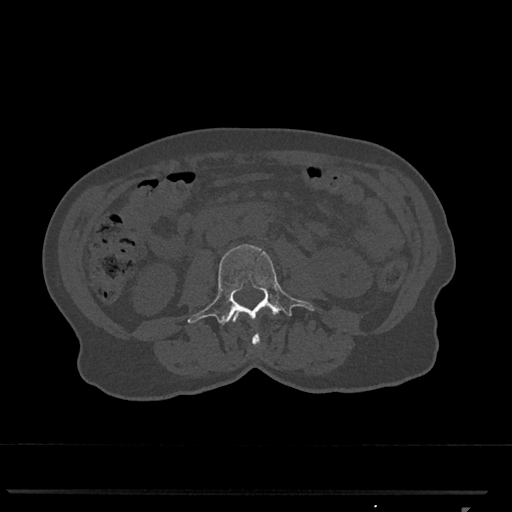
CT including the spine, one axial slice; bone window (W 1800 / L 400 HU); 0.5 mm slice thickness; 512 × 512 image matrix, field of view 380 × 380 mm. Patient: female, 62 years. From the clinical record (not read from this slice): primary cancer: renal.
Structures marked on this image (semi-automatic segmentation, software-assisted and operator-edited):
- L2 vertebra: box from (x=233, y=312) to (x=260, y=347) px
- L3 vertebra: (x=187, y=244)–(x=315, y=325)